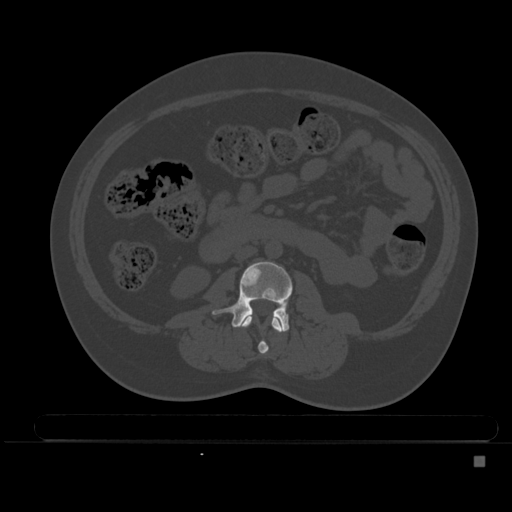
CT including the spine, one axial slice; slice 158 of 495 in the series (ordered by position); bone window (W 1800 / L 400 HU); 1.5 mm slice thickness; 512 × 512 image matrix, field of view 404 × 404 mm. Patient: female, 33 years. Case-level facts recorded for this patient, not image findings: primary cancer: breast.
Structures marked on this image (semi-automatic segmentation, software-assisted and operator-edited):
- L2 vertebra: bounding box [x1, y1, x2, y2] px = [239, 315, 284, 354]
- L3 vertebra: [212, 261, 293, 332]